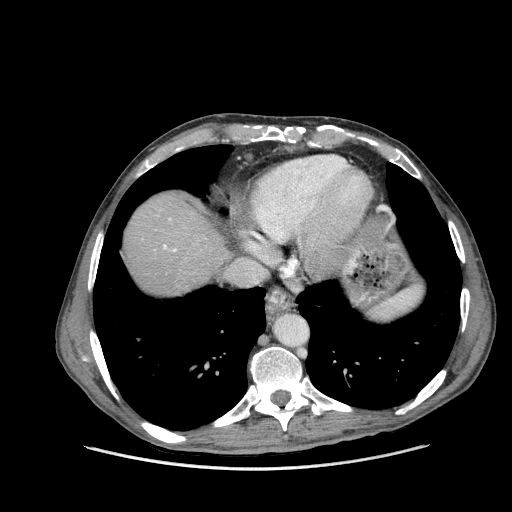
Contrast-enhanced abdominal CT (liver protocol), one axial slice. Position 137 of 162 along the scan axis. Reconstruction kernel STANDARD. 100 kVp. Soft-tissue window (W 400 / L 40 HU). 512 × 512 image matrix. Case-level facts recorded for this patient, not image findings: diagnosis: hepatocellular carcinoma (patient treated with transarterial chemoembolisation; whether this scan precedes or follows treatment is not stated here); TNM stage (as recorded): Stage-IIIA; Child-Pugh class: A.
Outlined on this slice (semi-automatically segmented with operator editing):
- abdominal aorta: bounding box (x1, y1, x2, y2) in pixels: (276, 315, 307, 347)
- liver parenchyma outside the tumour (the mass and vessels are separate outlines, so this box may not span the whole liver): (124, 194, 228, 294)
- liver vessels: (163, 245, 177, 252)